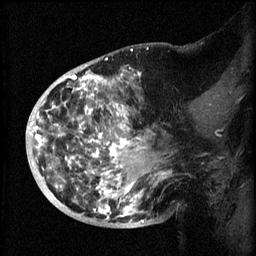
Breast MRI (dynamic contrast-enhanced), one sagittal slice. Position 27 of 60 along the scan axis. 3 images stored at this slice position (order not interpretable as contrast timing). 1.5 T. TE 4.2 ms, TR 8.2 ms. 2 mm slice thickness. 256 × 256 image matrix. Female patient, age 50 years.
Annotated regions visible in this slice (semi-automatically segmented with operator editing):
- analysis volume of interest (the breast-tissue region the enhancement analysis was run in; not a lesion): bounding box (x1, y1, x2, y2) in pixels: (44, 72, 172, 219)
- tumour enhancement mask (voxels above the 70 % enhancement threshold inside the analysis volume of interest): (44, 72, 168, 219)